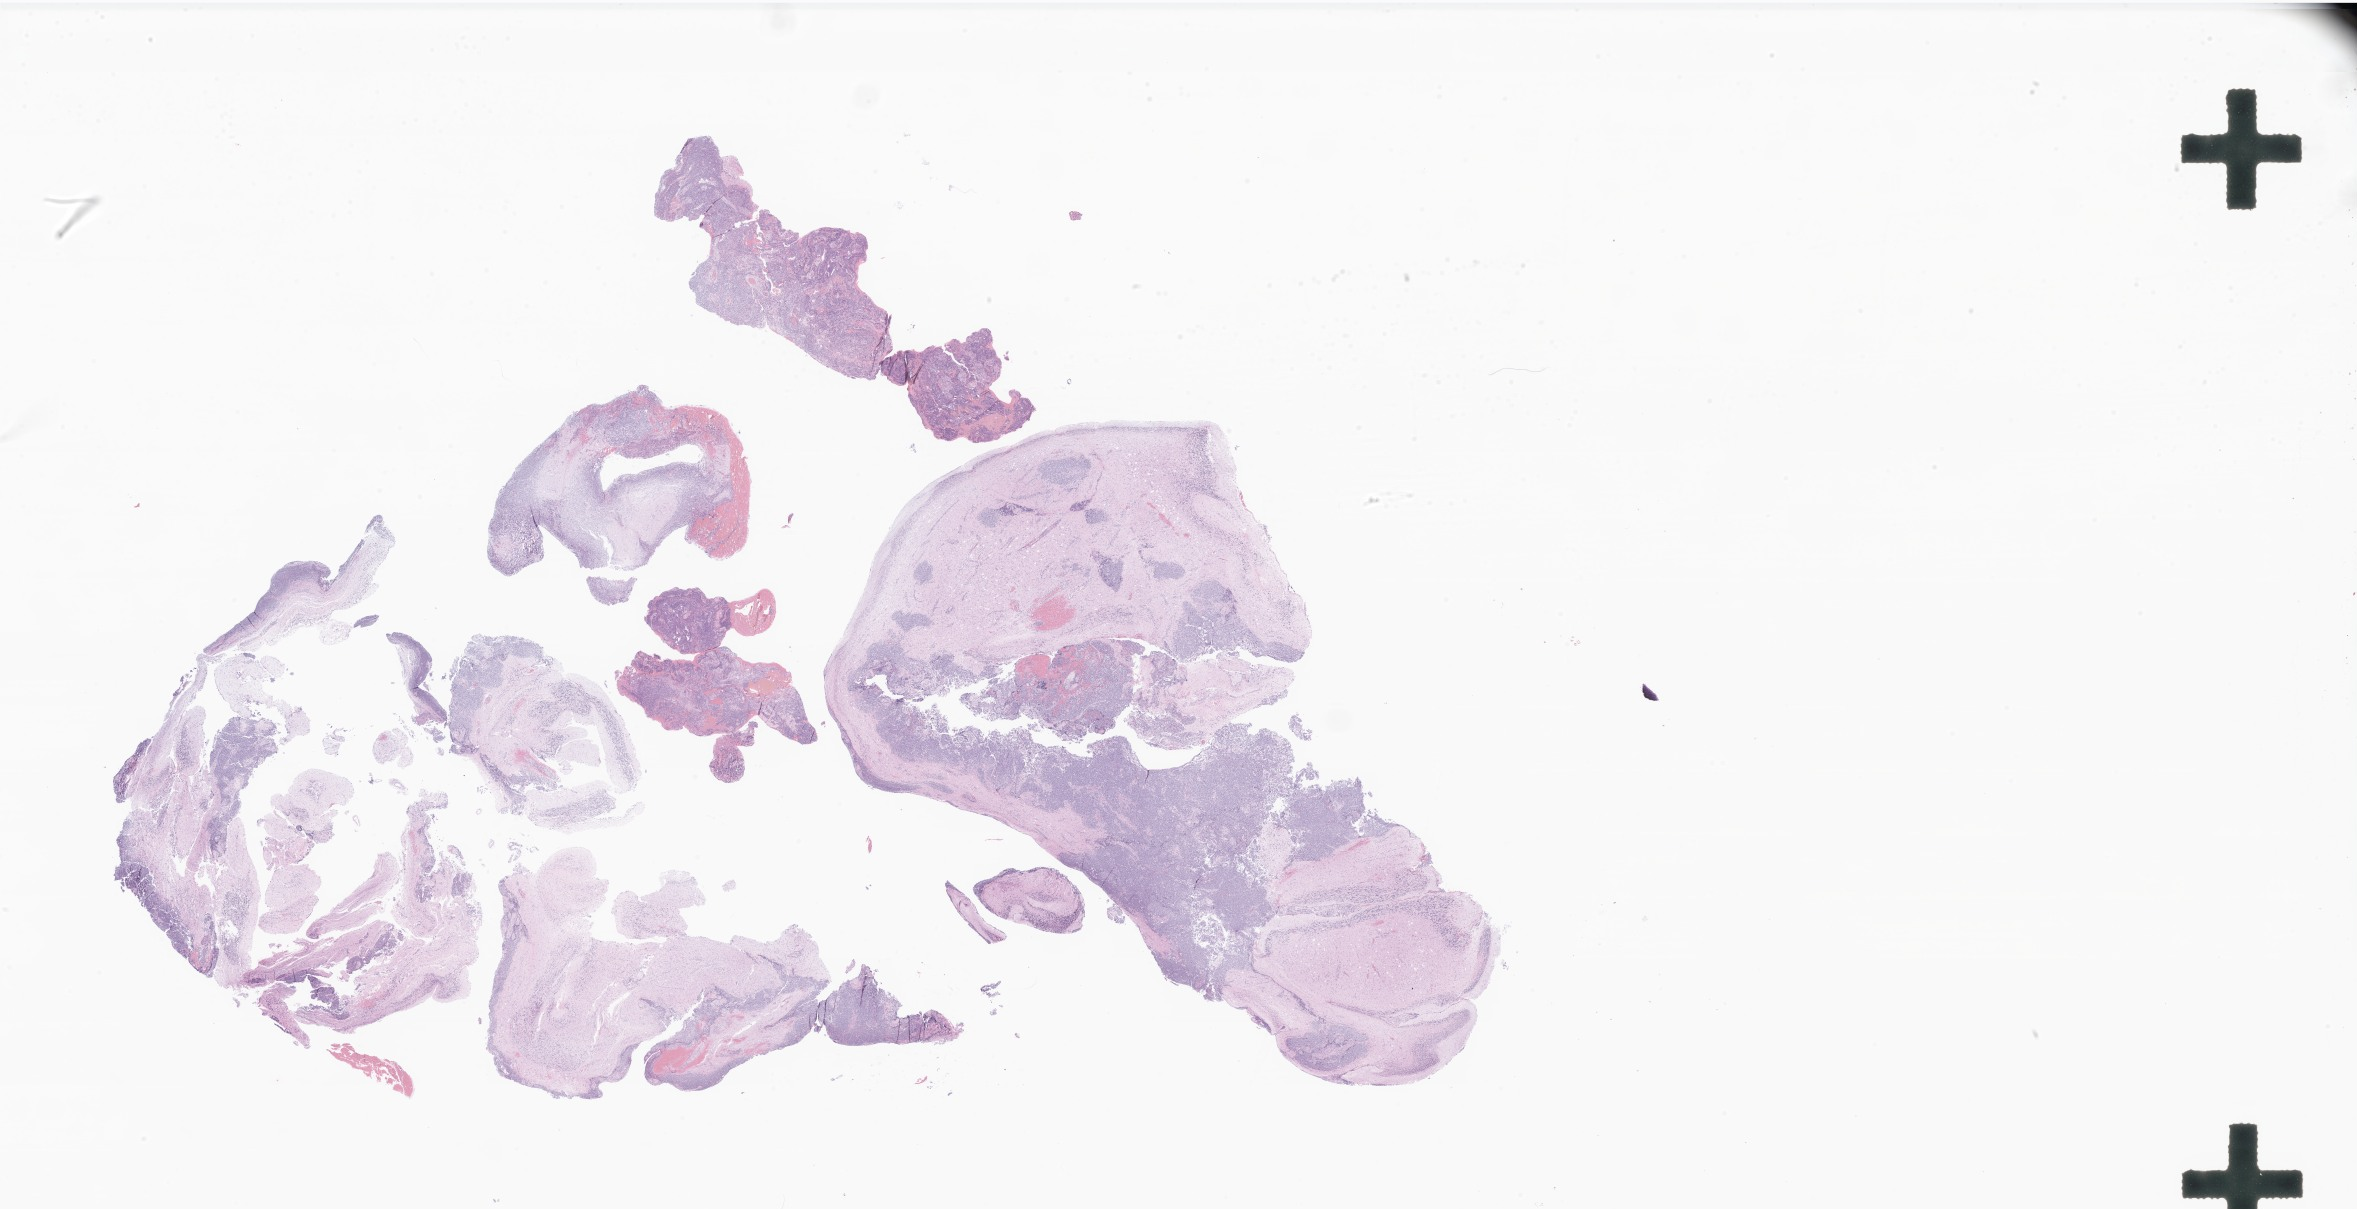
Digitized H&E-stained section of tumor tissue from the brain — a low-resolution overview of the entire scanned area, about 39.7 x 20.4 mm, formalin-fixed paraffin-embedded section. Patient male; age 170 months (14 years 2 months).
* diagnosis (ICD-O-3 morphology term): Medulloblastoma, NOS